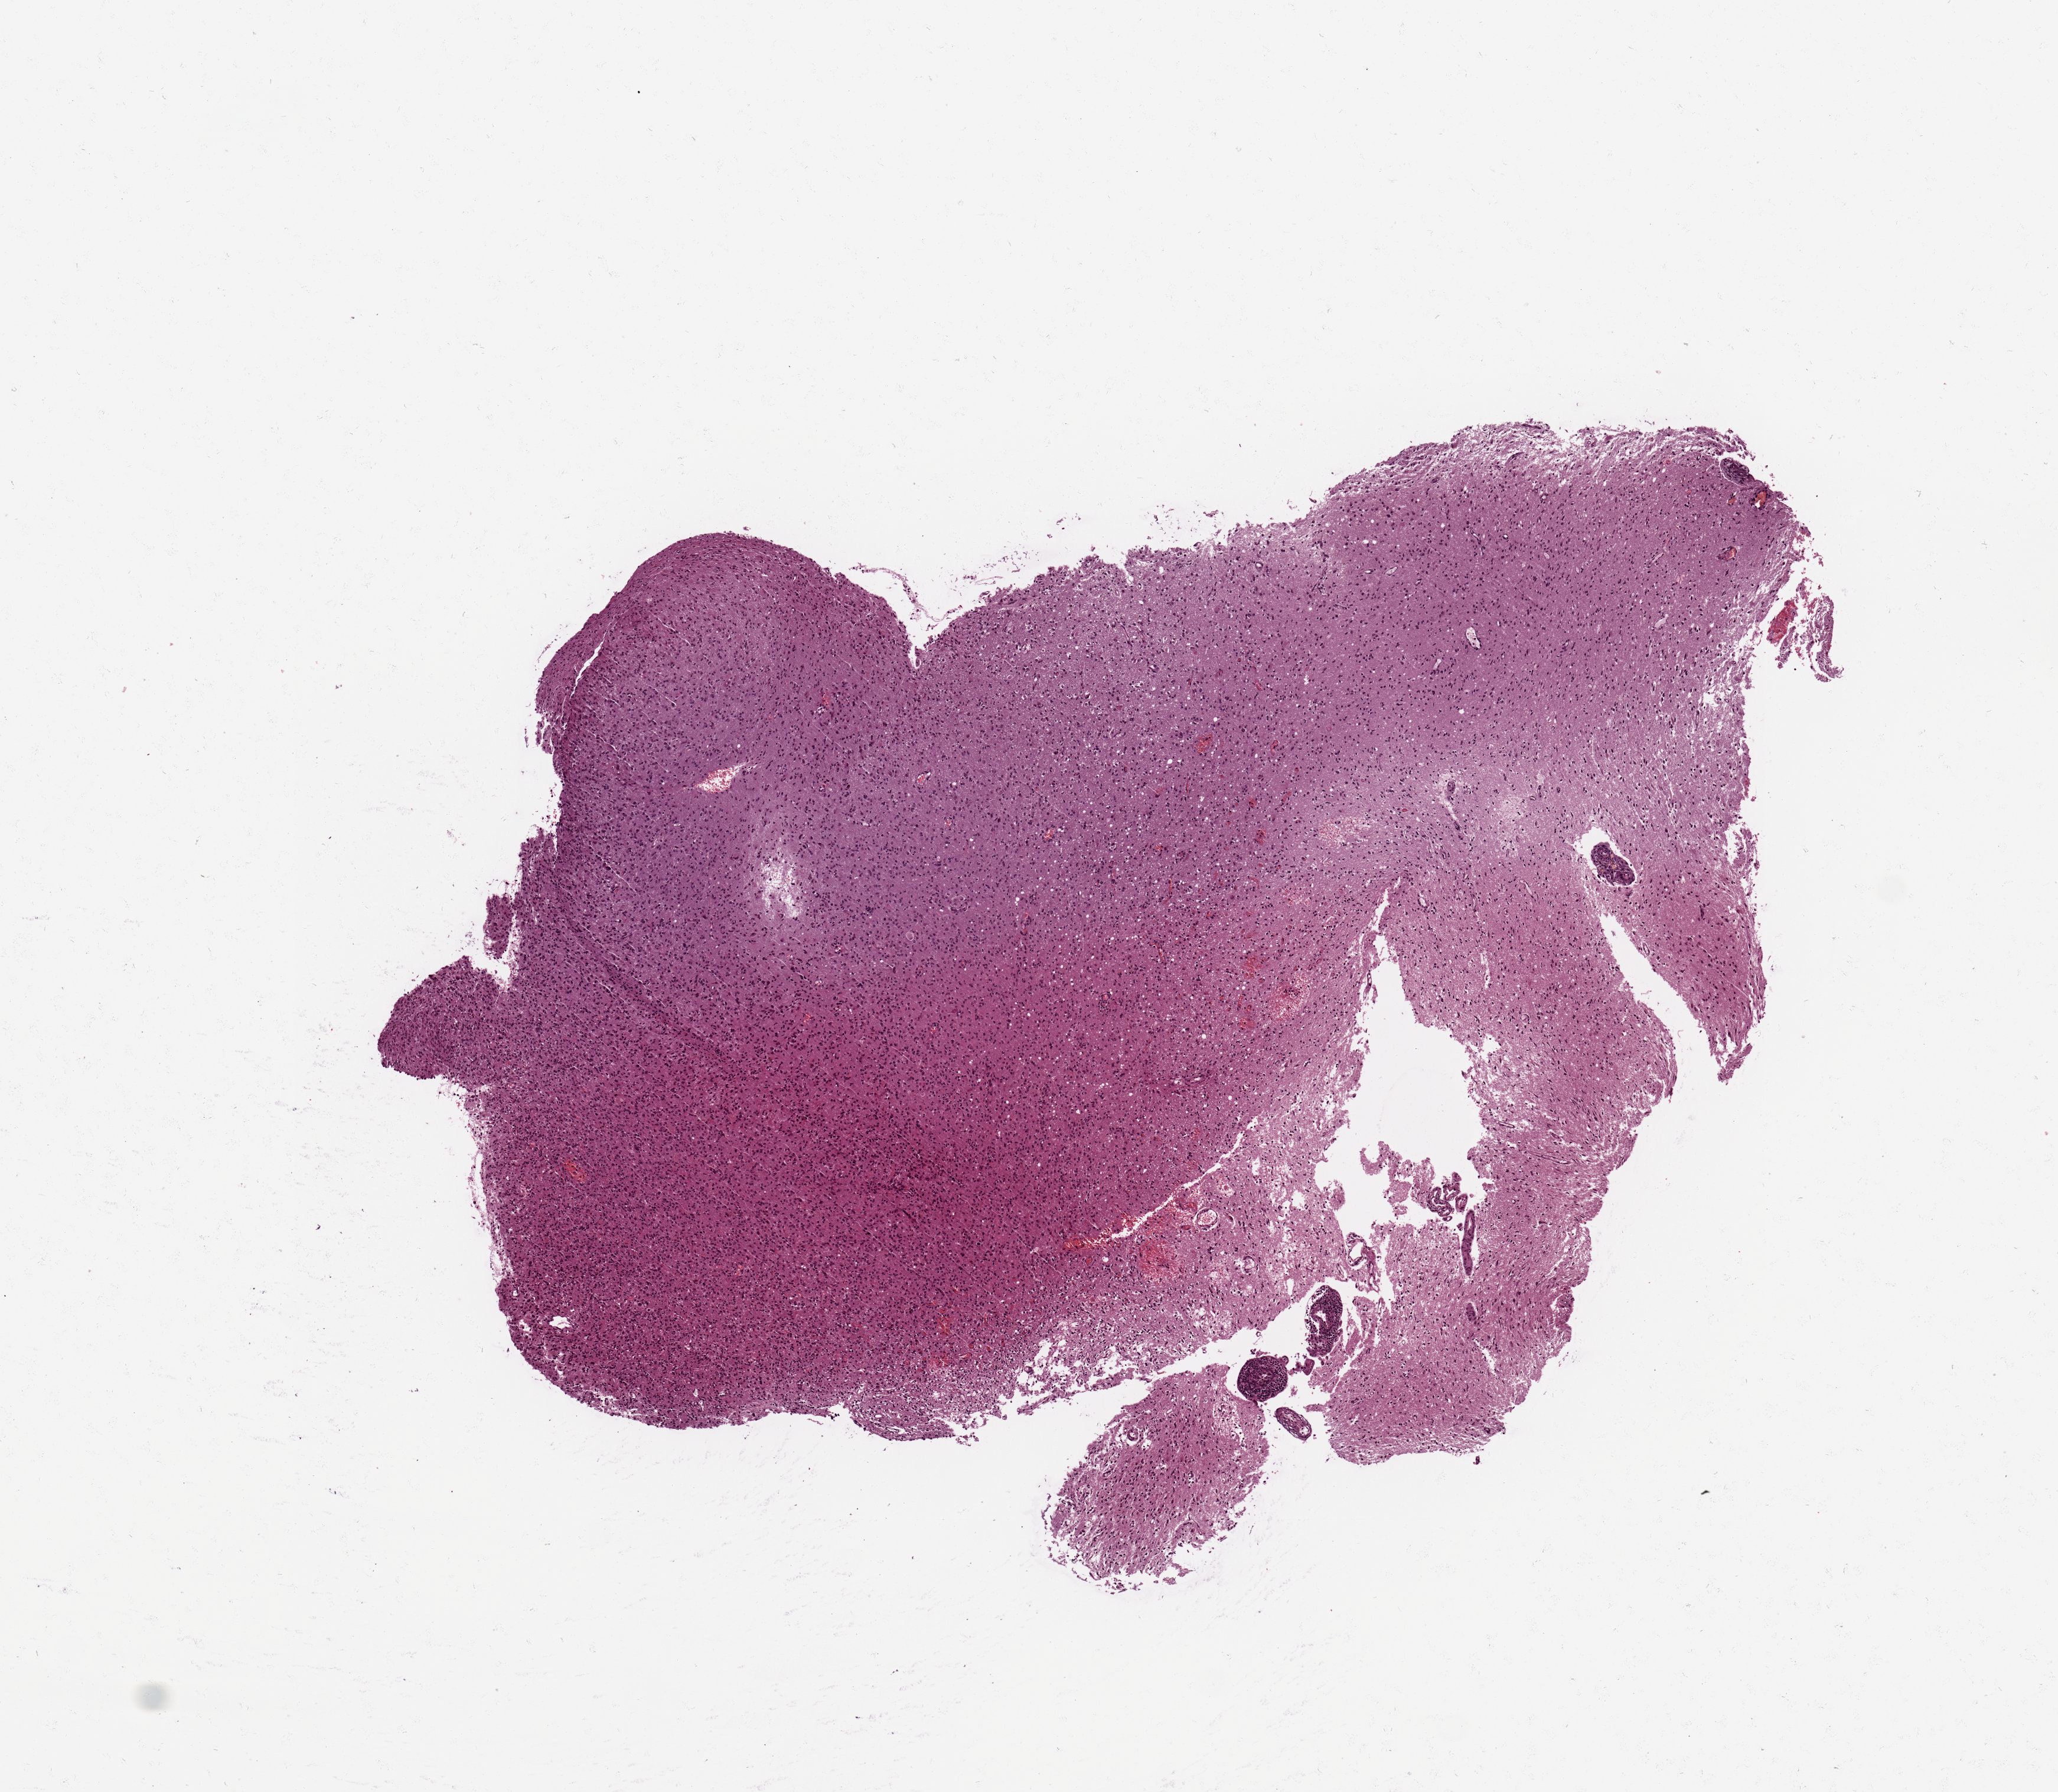
Whole-slide histology image, Hematoxylin and eosin (H&E) stained — low-resolution overview of the scanned area, about 6.9 x 6.0 mm. Tumour tissue sample, brain. Patient: male, age 49 years.
Diagnosis: Glioblastoma.